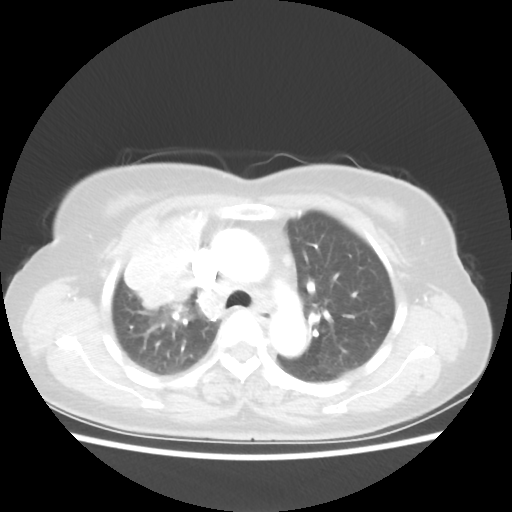
Chest CT, one axial slice. Slice 37 of 55 in the series (ordered by position). Reconstruction kernel STANDARD. Lung window (W 1500 / L -600 HU). 5 mm slice thickness. 512 × 512 image matrix, field of view 337 × 337 mm. Female patient, age 62 years. Case-level facts recorded for this patient, not image findings: clinical TNM (as recorded): T4 N3 M0.
Outlined on this slice (rectangle marked by the reading radiologist):
- lung tumour (recorded histology: squamous cell carcinoma): bounding box [x1, y1, x2, y2] px = [120, 208, 213, 308]